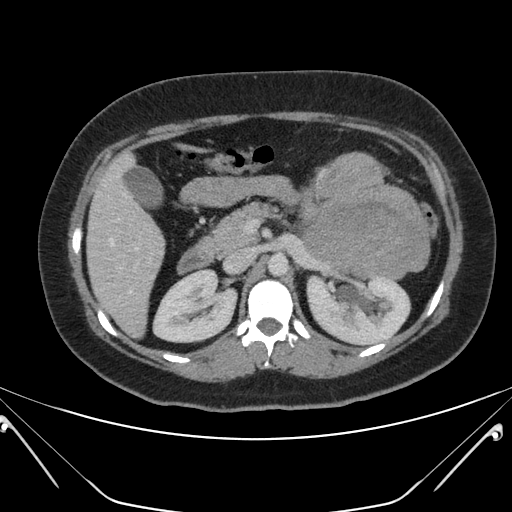
Contrast-enhanced abdominal CT, one axial slice; slice 120 of 168 in the series (ordered by position); intravenous contrast given; soft-tissue window (W 400 / L 40 HU); 512 × 512 image matrix, field of view 394 × 394 mm. Female patient, age 26 years. Case-level facts recorded for this patient, not image findings: diagnosis: adrenocortical carcinoma; tumour side: left adrenal; tumour size at pathology: 28 cm; Ki-67 index: 20 %; stage (as recorded): 2.
Annotated regions visible in this slice (semi-automatic segmentation, software-assisted and operator-edited):
- mass: bounding box [x1, y1, x2, y2] px = [302, 154, 427, 276]